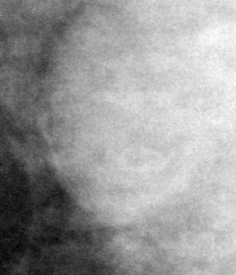
Region of interest cut from a scanned film mammogram (one marked finding), left breast, CC view, BI-RADS breast density category 3 (scale 1–4).
- Finding: mass, shape oval, margins circumscribed; BI-RADS assessment category 3; pathology result (as recorded, not read from the image): benign.